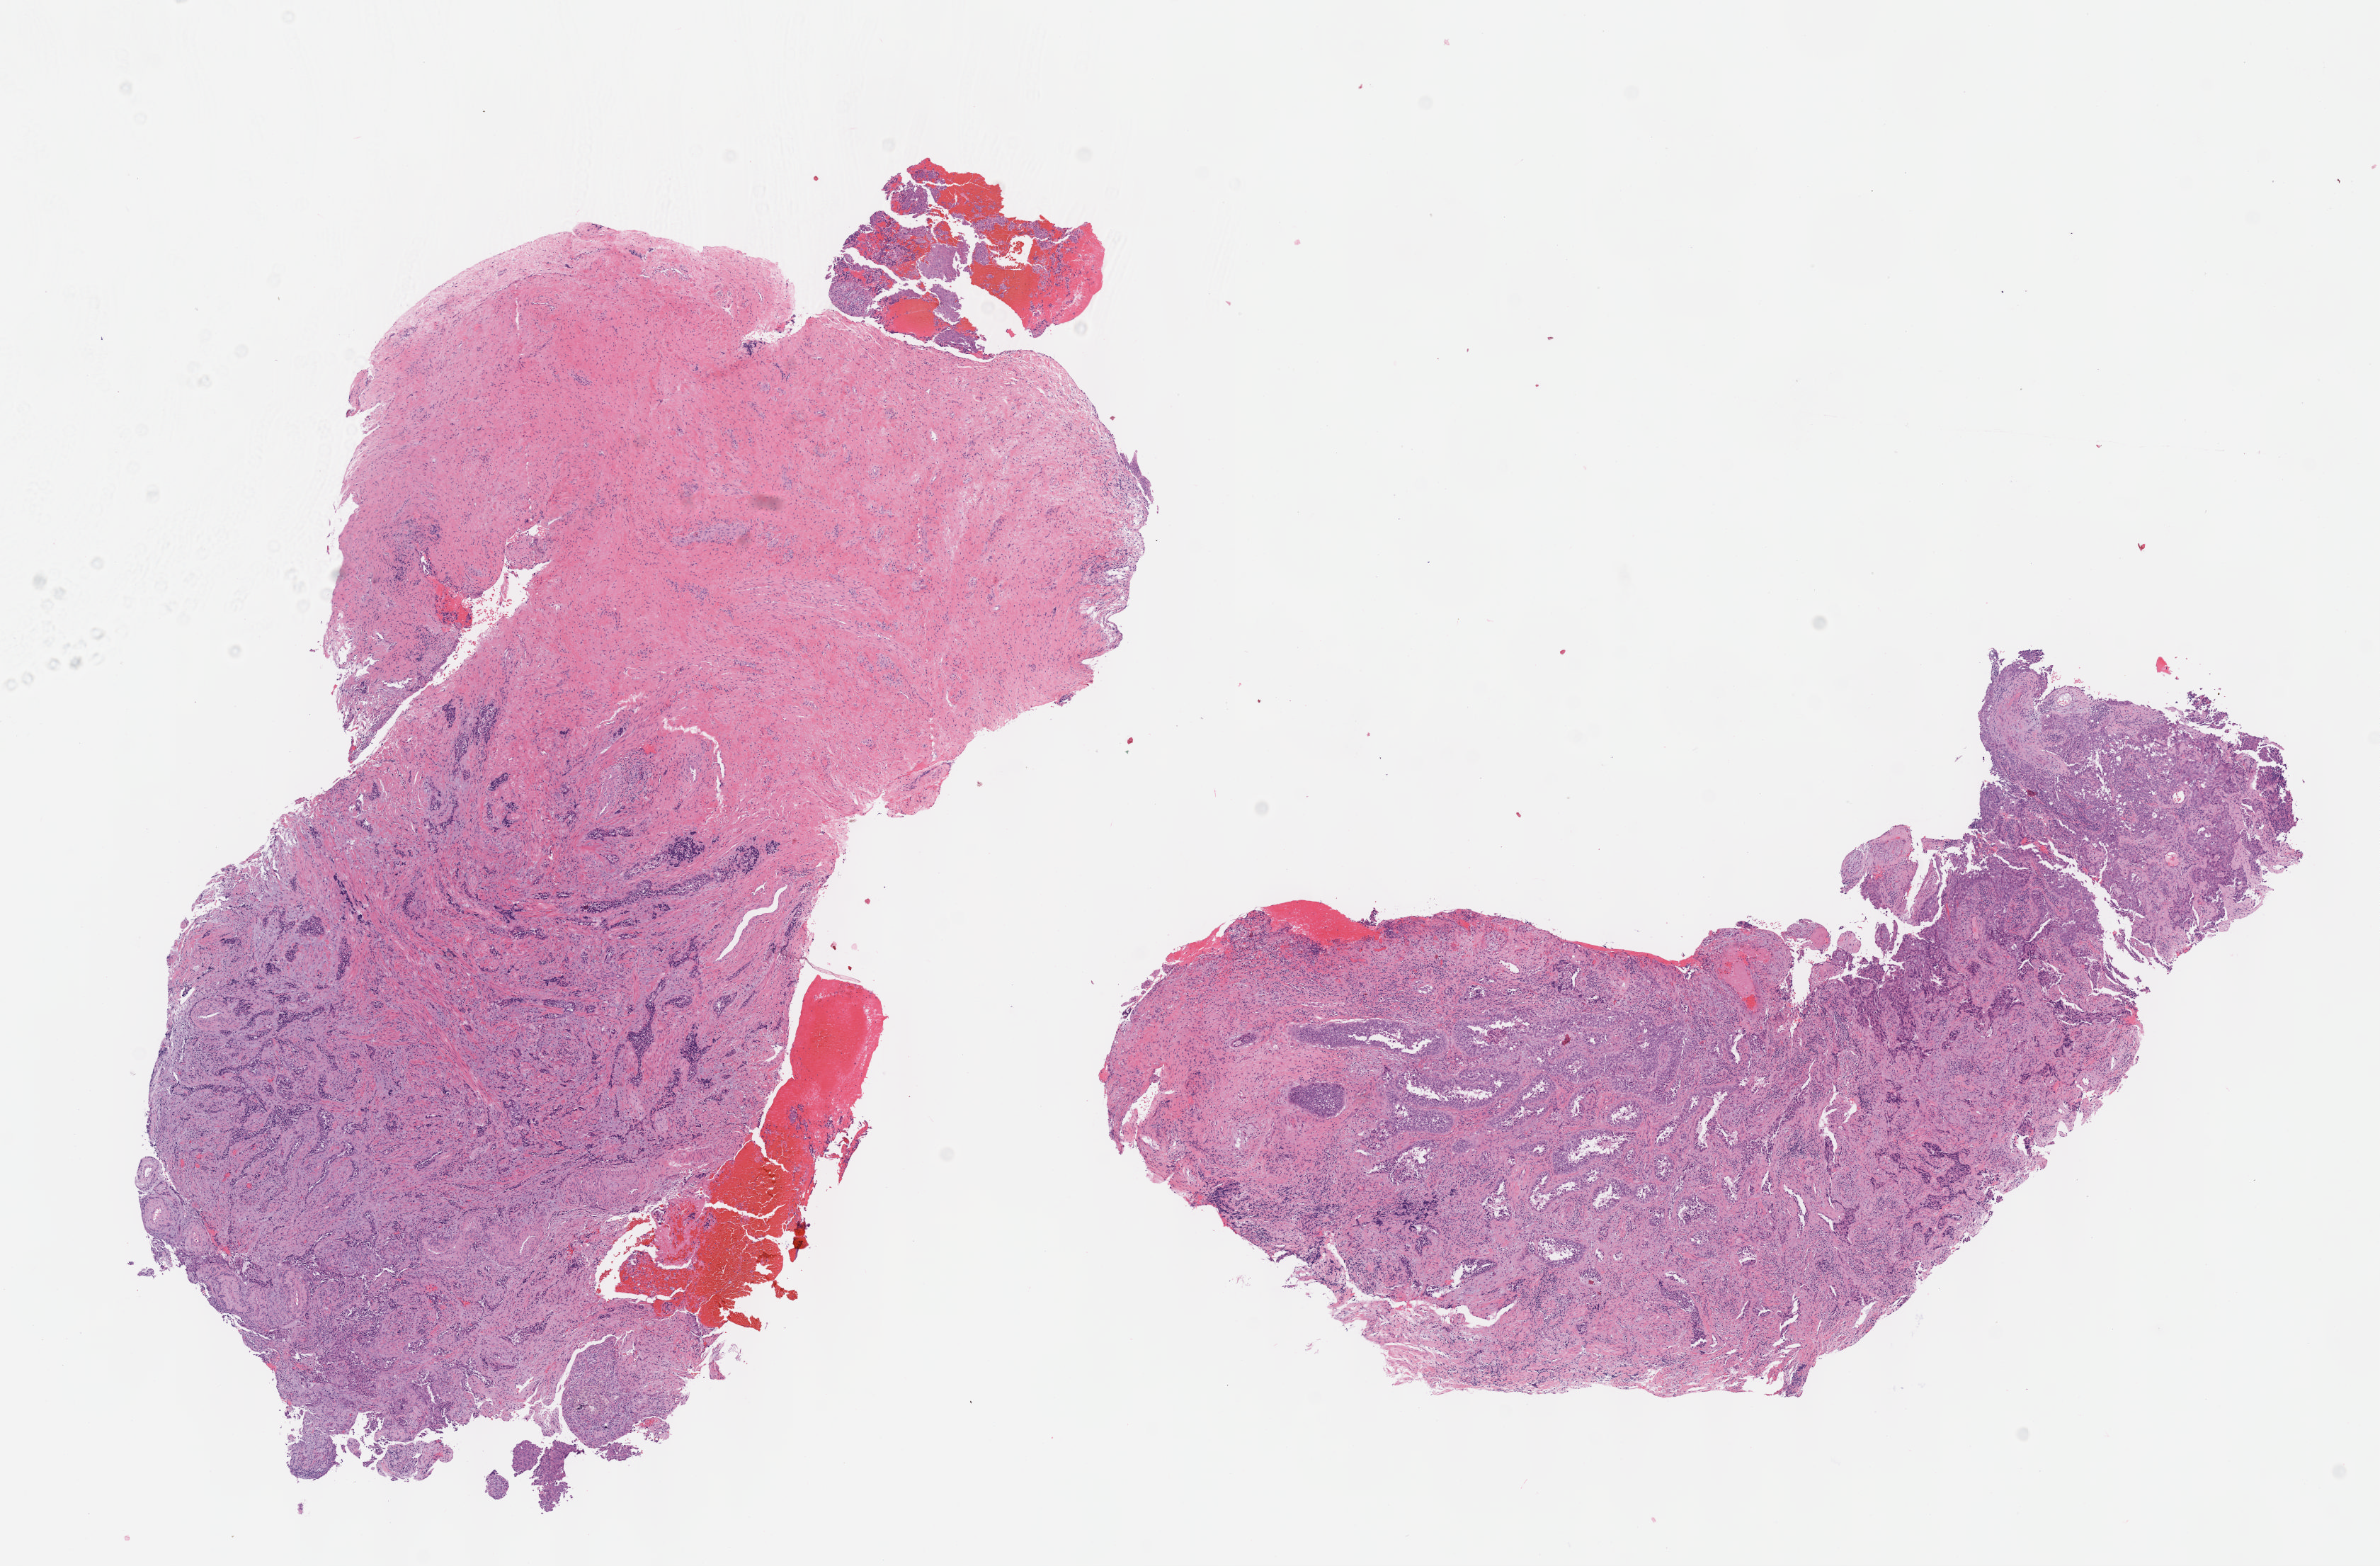
Hematoxylin and eosin (H&E) stained whole-slide image — a low-resolution overview of the entire scanned area, about 13.6 x 8.9 mm (from a 40x scan); formalin-fixed paraffin-embedded (FFPE) diagnostic section; primary tumour sample from the cervix. Female patient; age at initial diagnosis 64 years. Histologic grade: G2 (moderately differentiated).
Histologic diagnosis: Squamous cell carcinoma, NOS (cervix uteri). FIGO stage: IIIB.